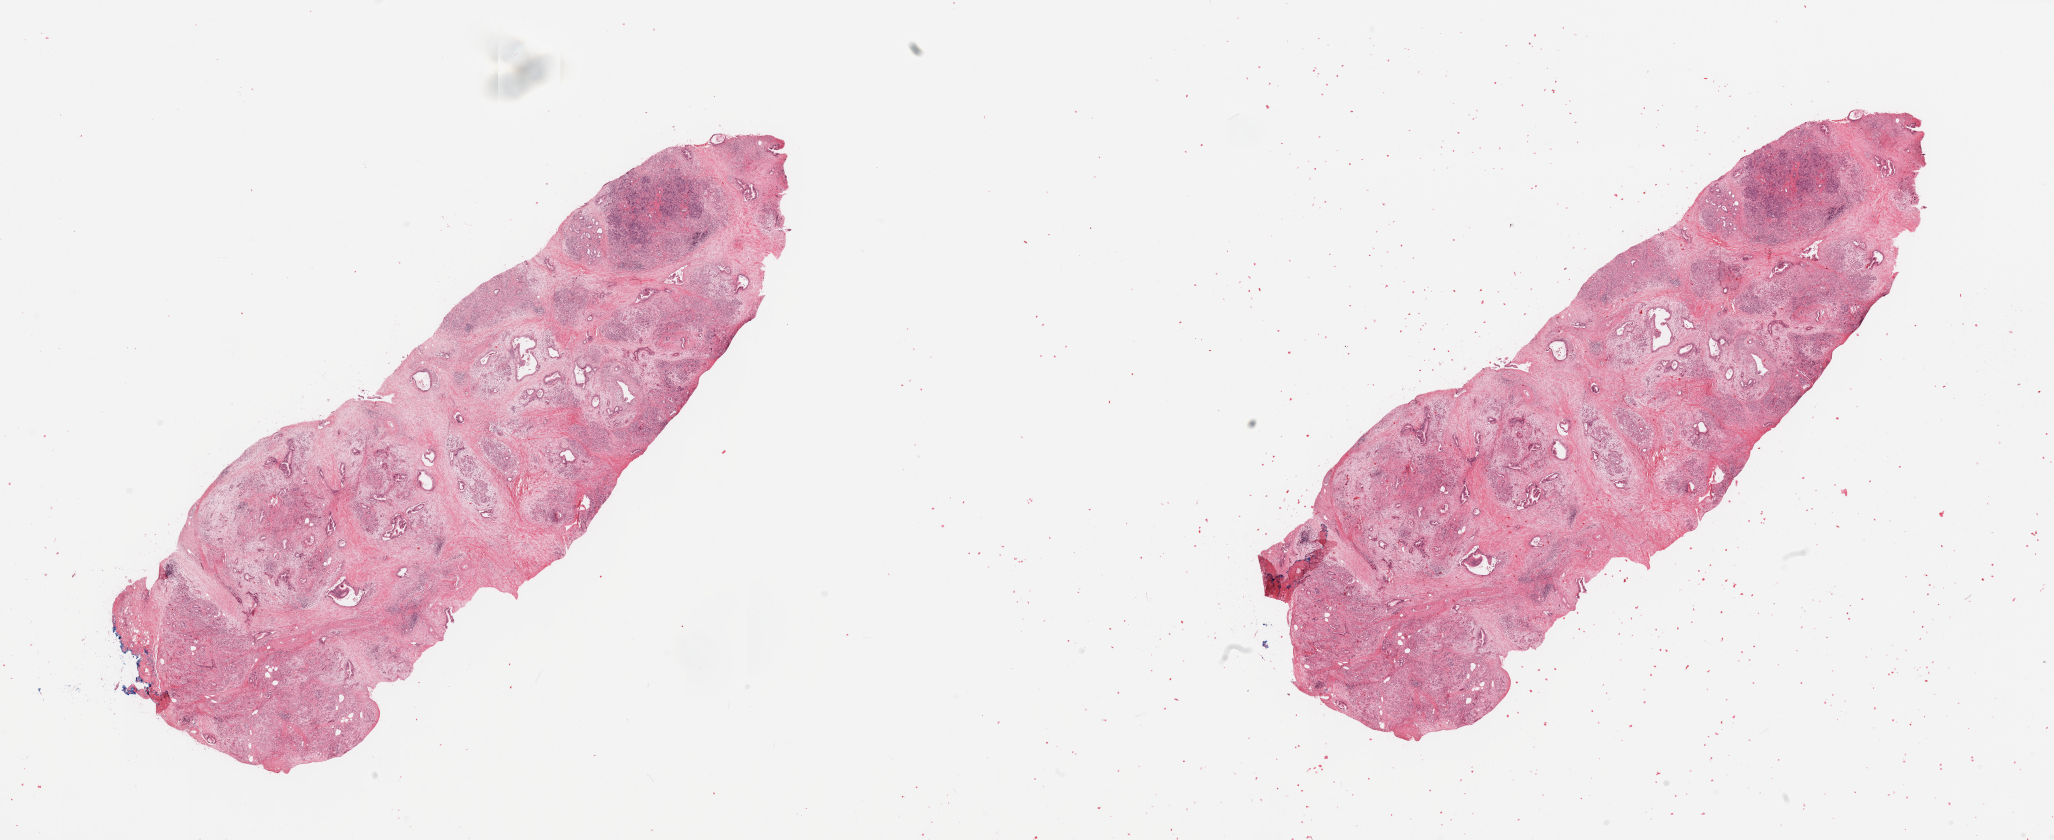
Whole-slide histology image, H&E — shown as a low-resolution overview of the whole scanned area (about 32.5 x 13.3 mm, acquisition: 20x scan), tumour tissue sample, sampled site: pancreas. 77-year-old female patient. Histologic grade: G2 (moderately differentiated). Pathologist review of this section (percent, as recorded): tumour nuclei 10%, necrosis 1%.
Histologic diagnosis: Infiltrating duct carcinoma, NOS. AJCC pathologic stage: IIB. Primary tumour site (as recorded): head.